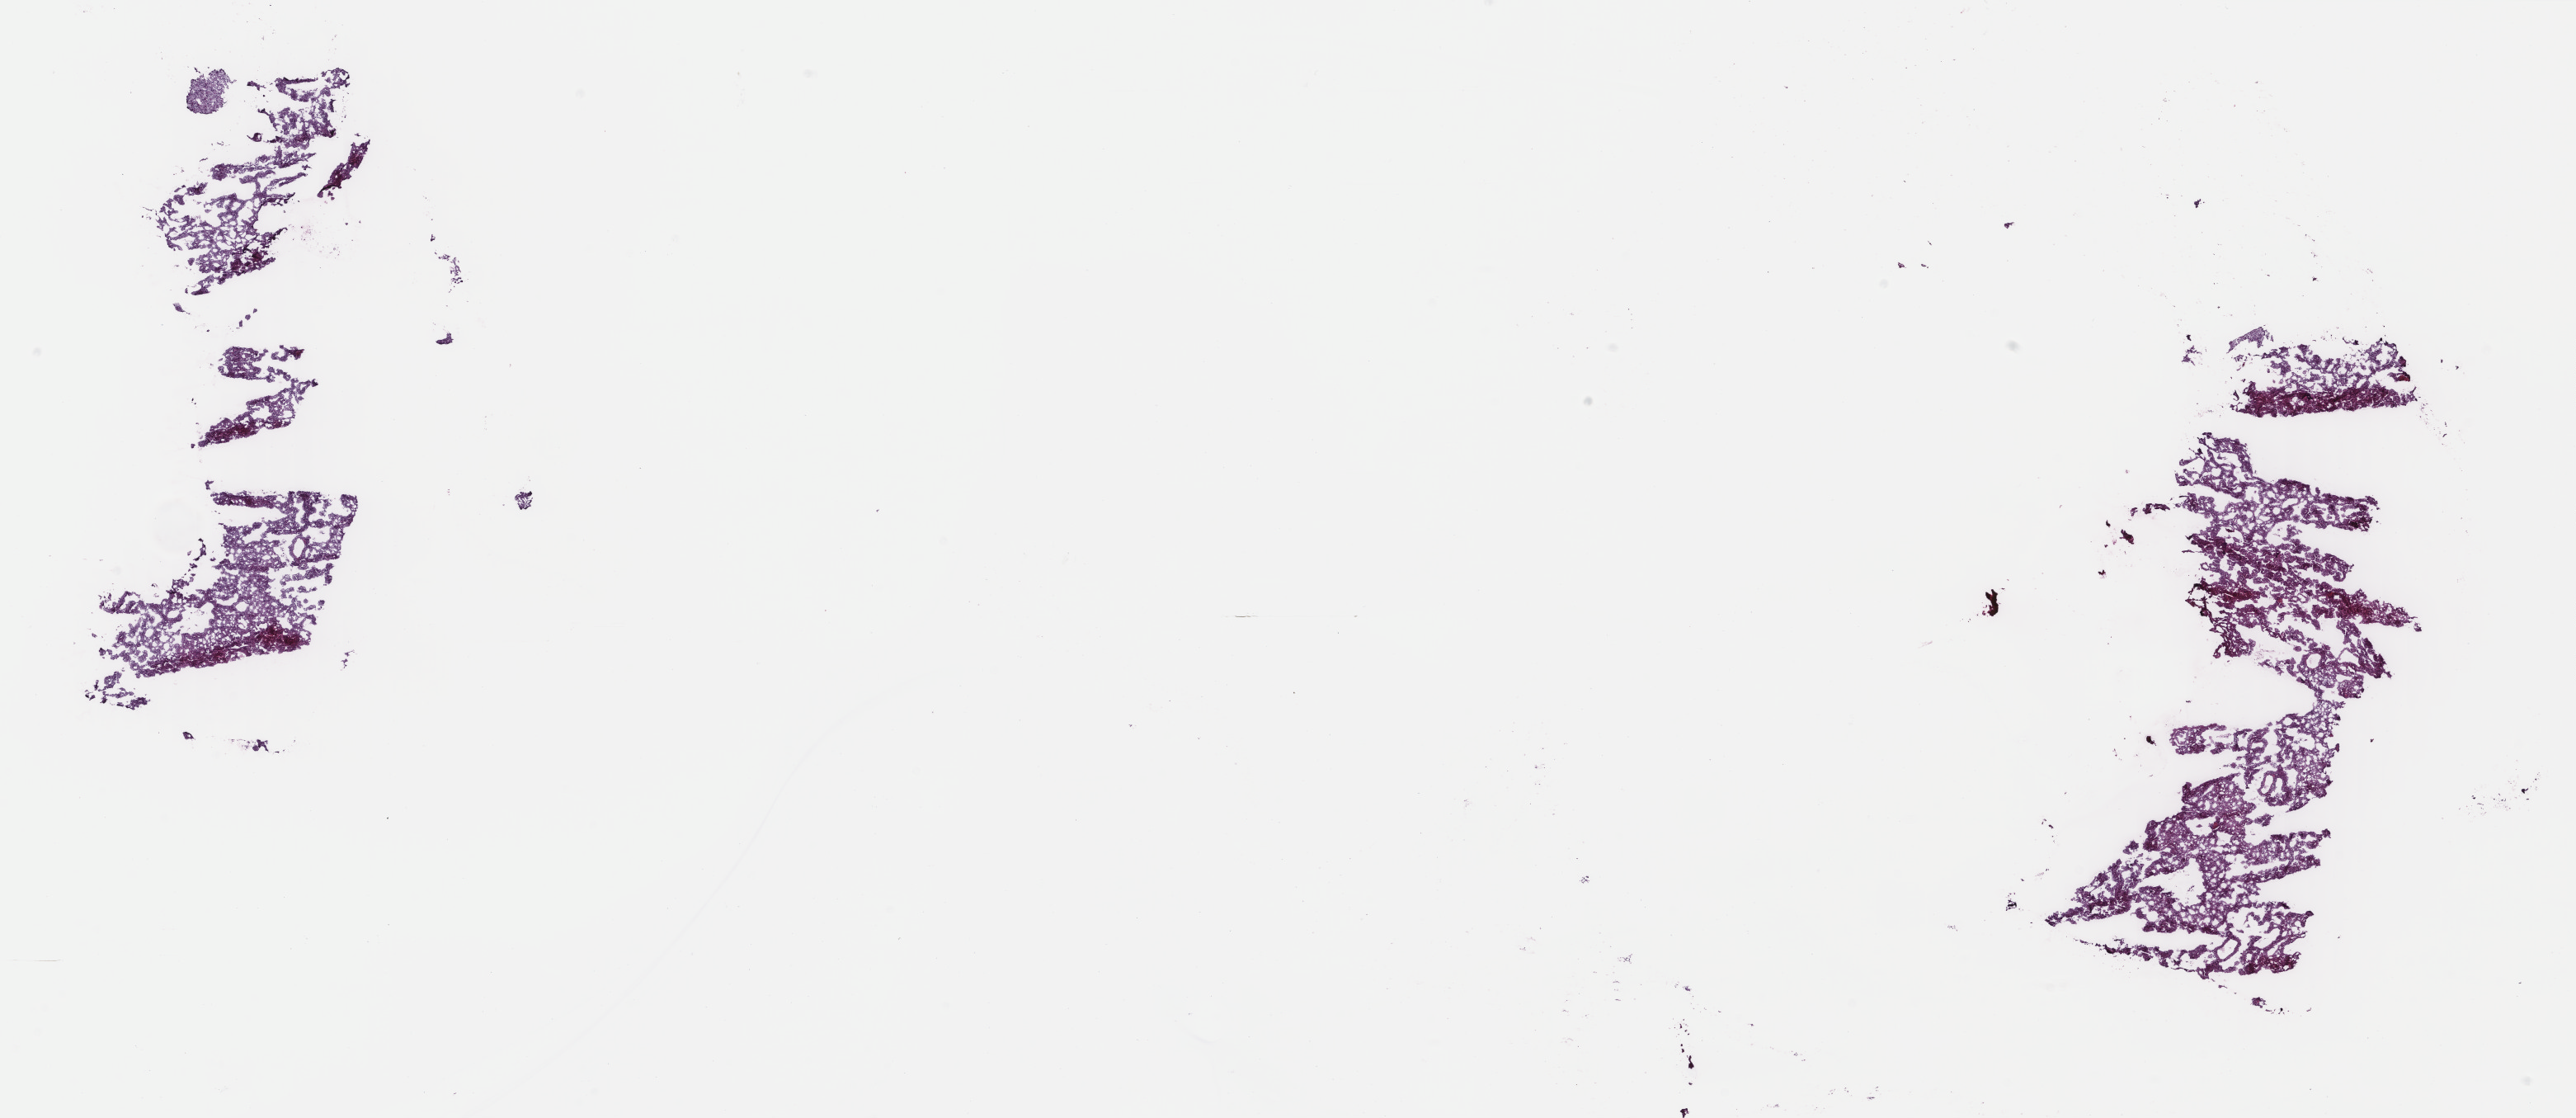
Digitized H&E tissue section (whole slide), shown as a low-resolution overview of the whole scanned area (about 24.8 x 10.8 mm); frozen section; liver, primary tumour sample. Female, age 72 years at initial diagnosis. Histologic grade: G2 (moderately differentiated). Slide review estimates, as recorded: tumour cells 100%, tumour nuclei 97%, normal cells 0%, stromal cells 0%, necrosis 0%. Inflammatory infiltration, as recorded: lymphocyte infiltration 0%, monocyte infiltration 0%, neutrophil infiltration 0%.
• AJCC pathologic stage: II (4th edition)
• histologic diagnosis: Hepatocellular carcinoma, NOS